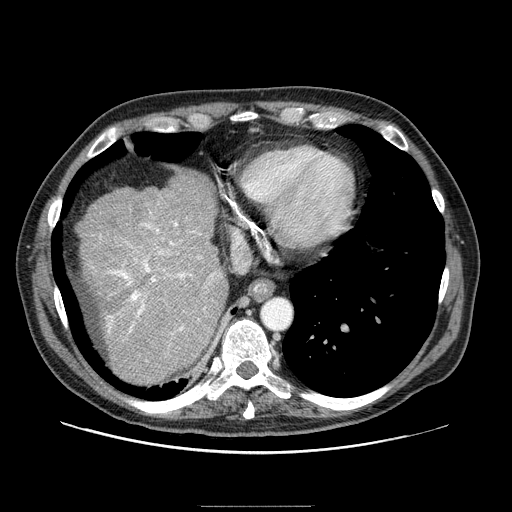
Contrast-enhanced abdominal CT (liver protocol), one axial slice; slice 75 of 99 in the series (ordered by position); reconstruction kernel STANDARD; one of 2 acquisitions stored at this slice position; soft-tissue window (W 400 / L 40 HU); 2.5 mm slice thickness; 512 × 512 image matrix, field of view 400 × 400 mm. From the clinical record (not read from this slice): diagnosis: hepatocellular carcinoma (patient treated with transarterial chemoembolisation; whether this scan precedes or follows treatment is not stated here); TNM stage (as recorded): Stage-II; Child-Pugh class: A; tumour differentiation: well differentiated; tumour nodularity: multinodular.
Outlined on this slice (semi-automatic segmentation, software-assisted and operator-edited):
- liver parenchyma outside the tumour (the mass and vessels are separate outlines, so this box may not span the whole liver): box from (x=80, y=174) to (x=228, y=384) px
- liver vessels: (x=107, y=212)–(x=216, y=334)